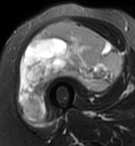
MRI of an extremity soft-tissue mass, one axial slice; slice 44 of 95 in the series (ordered by position); T2-weighted fat-saturated; MR volume resampled by the dataset authors to the PET/CT grid (not the native acquisition matrix); 3.27 mm slice thickness; 135 × 146 image matrix, field of view 132 × 143 mm. Female patient. From the clinical record (not read from this slice): histological type: pleiomorphic undifferentiated sarcoma; grade: high; site of the primary tumour: right quadricep.
Outlined on this slice (expert contour drawn on MRI and transferred to this co-registered scan by the dataset authors):
- gross tumour volume including surrounding oedema: bounding box <19,20,122,121> (left, top, right, bottom; pixels)
- gross tumour volume (mass): <19,20,122,121>